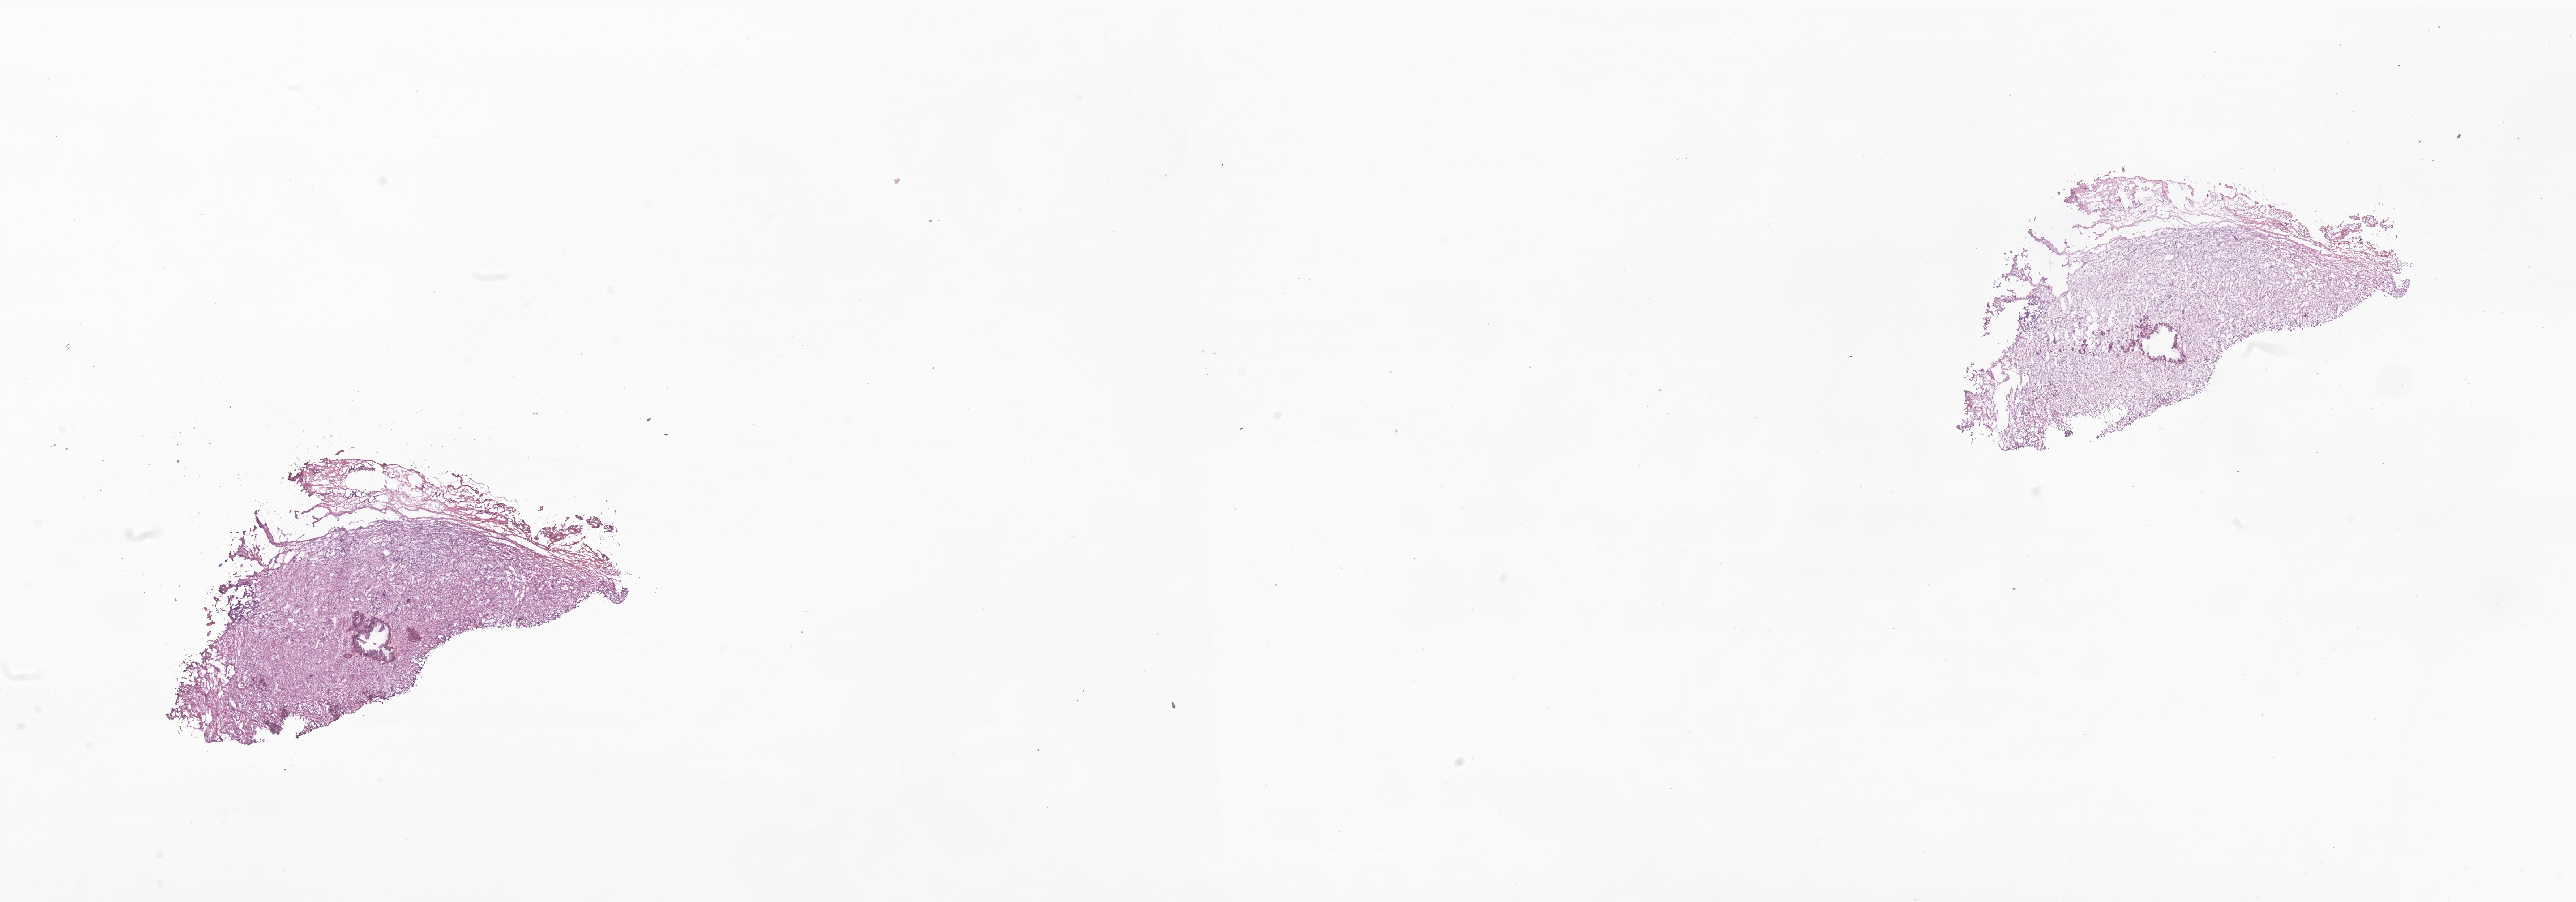
Digitized haematoxylin and eosin-stained section of tumor tissue from the adrenal gland — low-resolution overview of the scanned area, about 30.0 x 10.5 mm, cryosection (OCT / tissue freezing medium). Male patient, age 36 months (3 years).
Recorded diagnosis: Neuroblastoma, NOS.